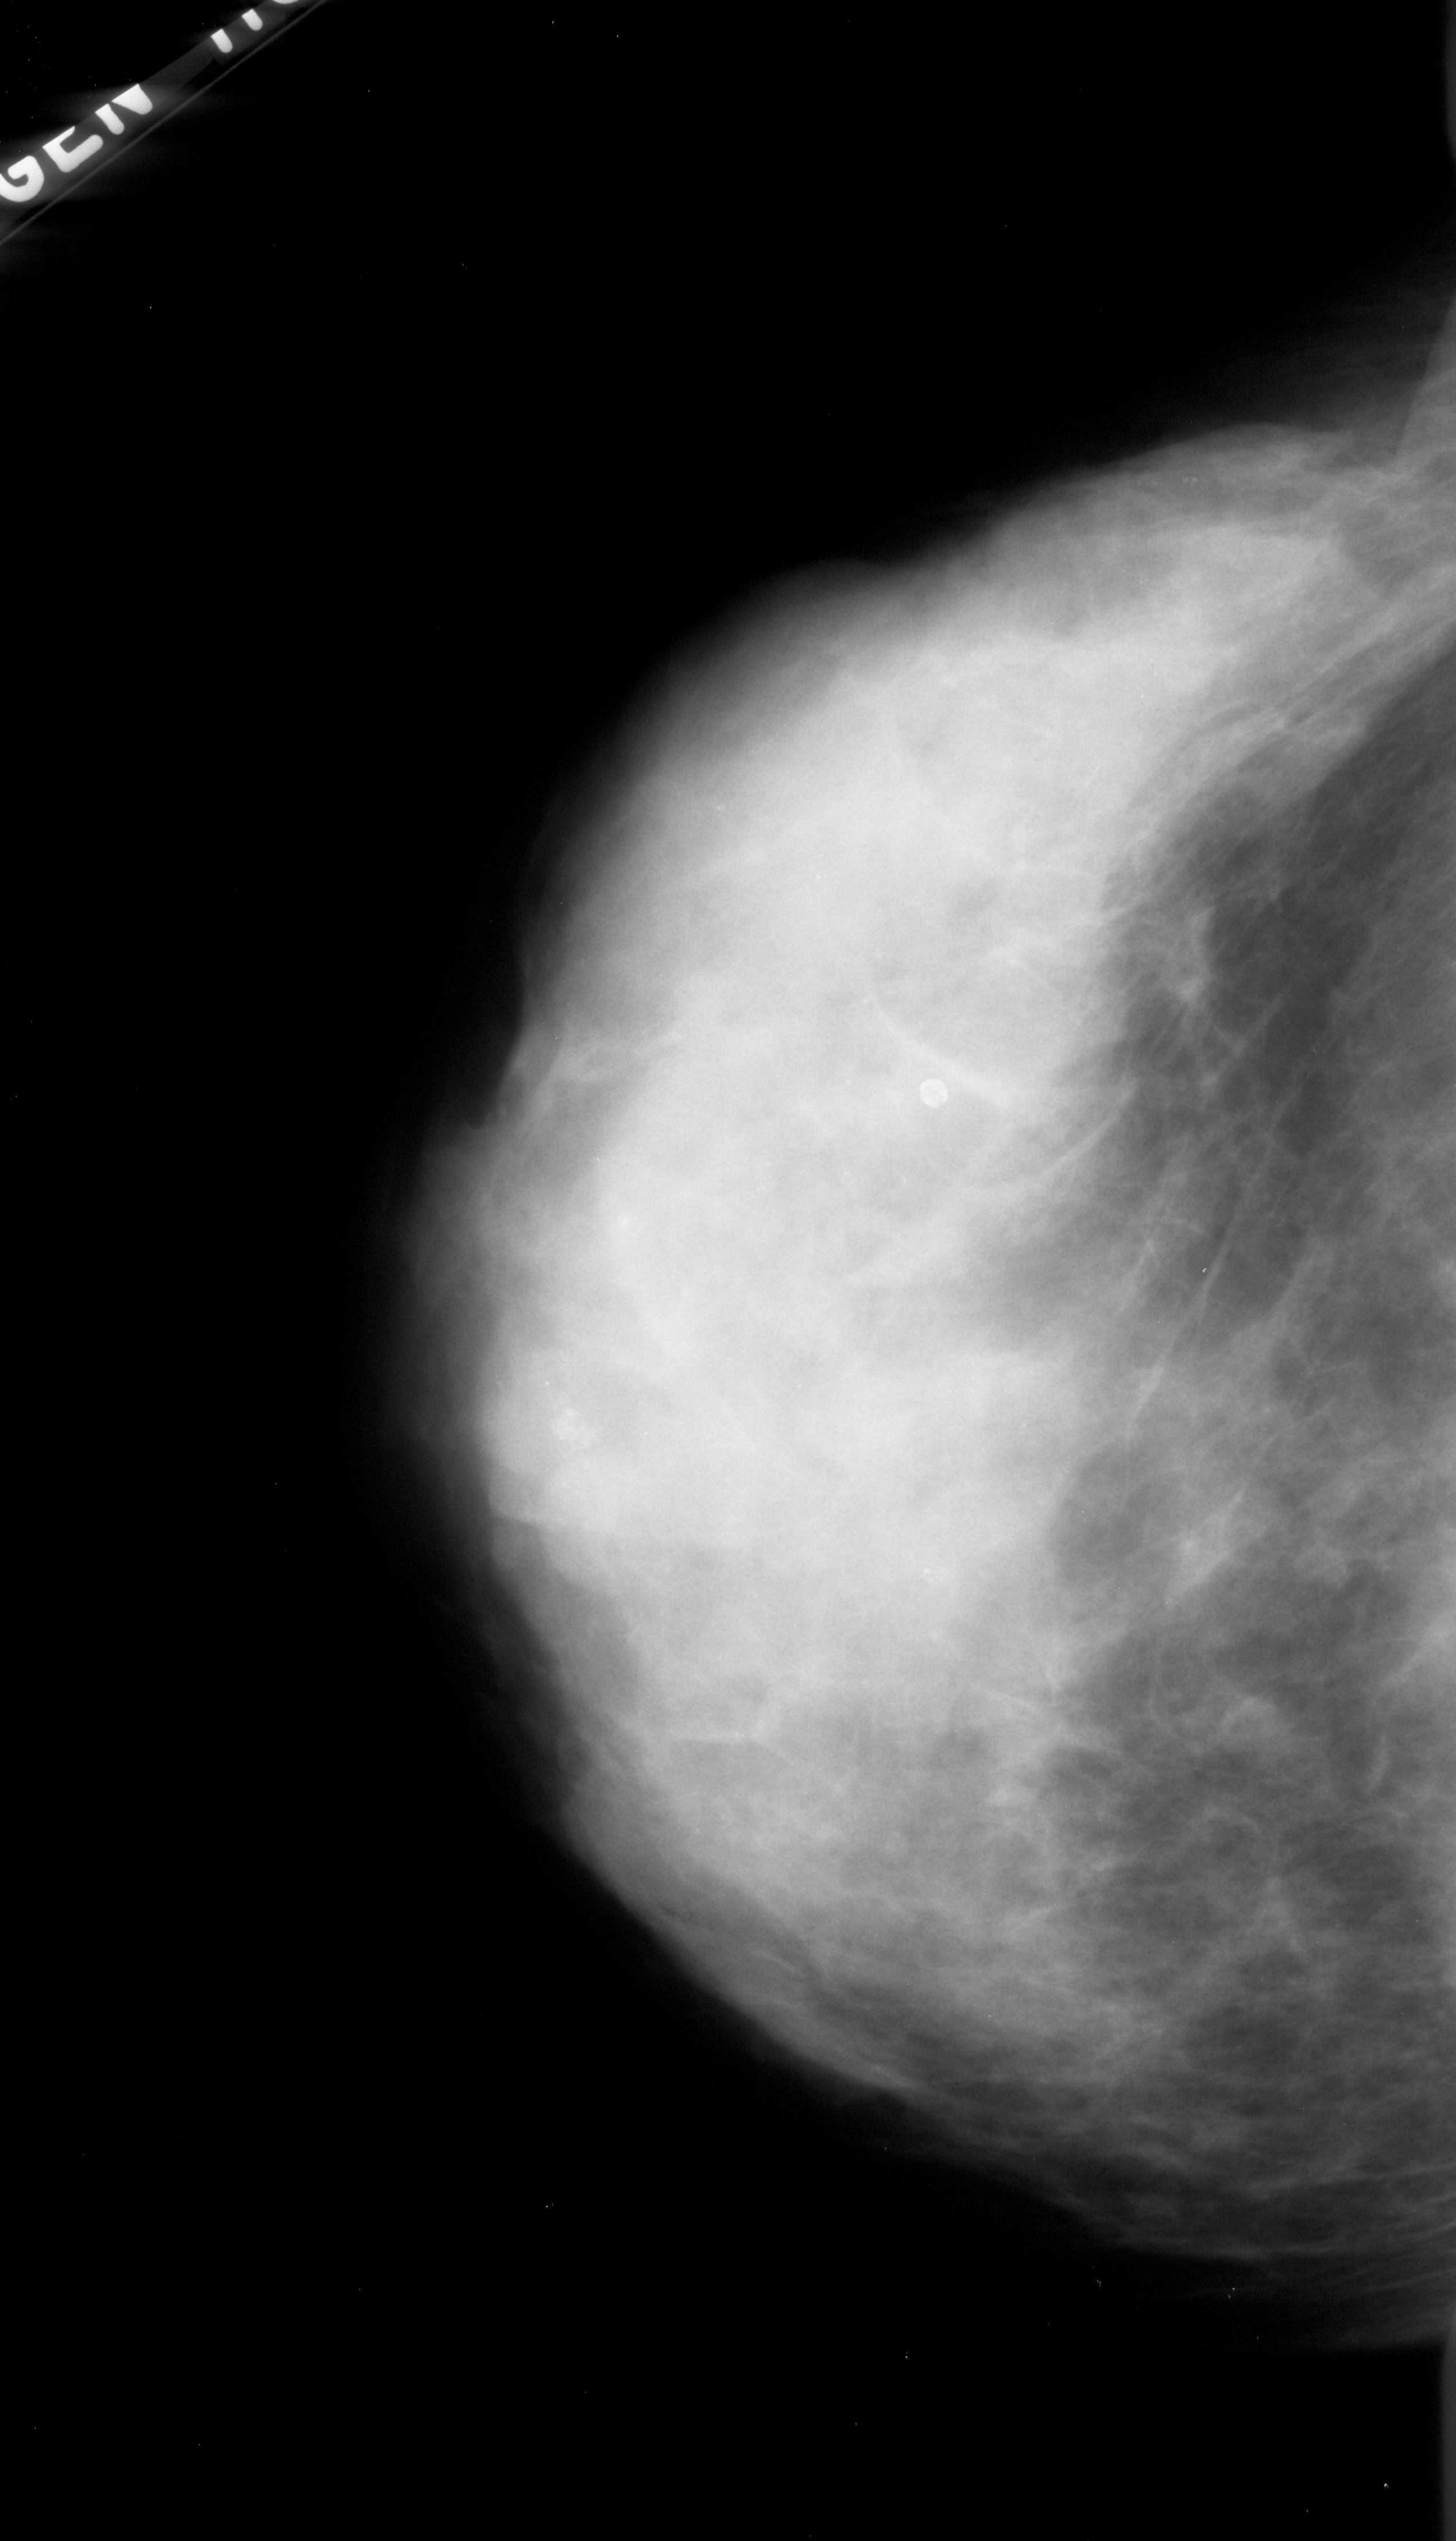
Scanned film-screen mammogram; left breast; craniocaudal (CC) view; BI-RADS breast density category 4 (scale 1–4).
Calcifications, morphology amorphous, distribution clustered; BI-RADS assessment category 4; subtlety rating 2 on a 1 (subtle) to 5 (obvious) scale; pathology result (as recorded, not read from the image): malignant.